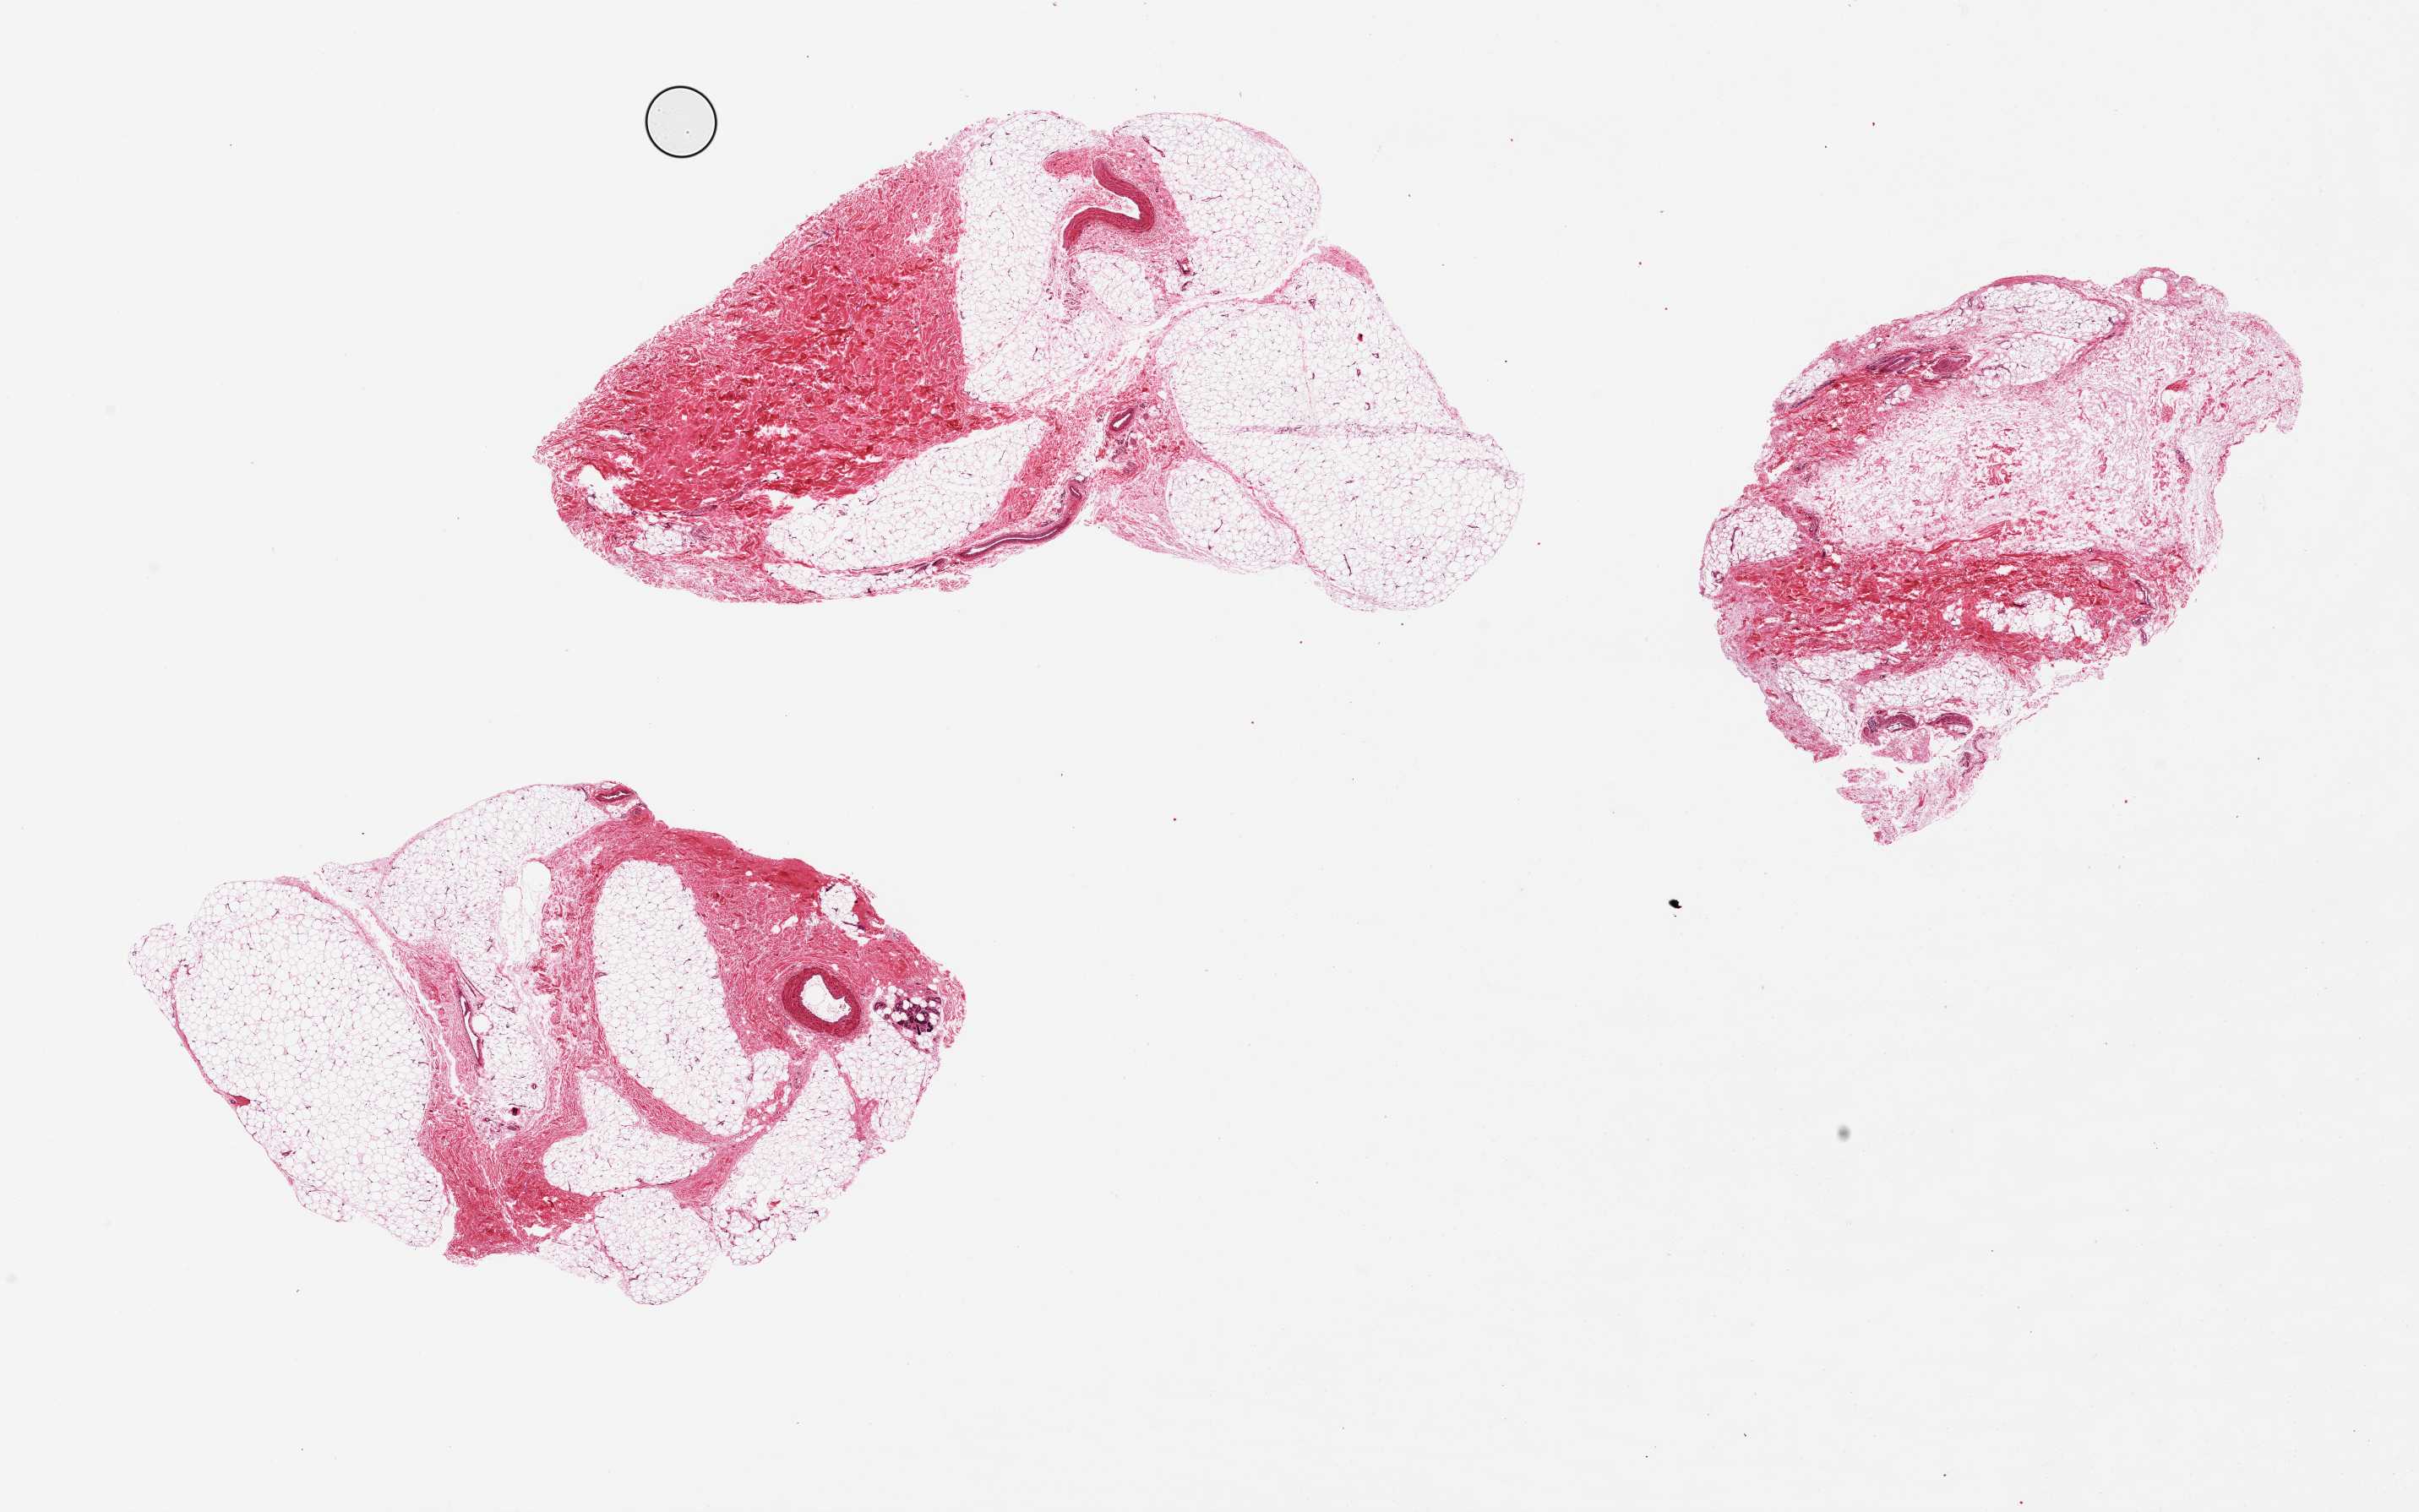
Whole-slide image, H&E stain, brightfield — a low-resolution overview of the entire scanned area, about 22.6 x 14.2 mm (acquisition: 20x scan), PAXgene-fixed paraffin-embedded (PFPE) section, sampled site (target tissue): tibial nerve, tissue donor sample. Donor sex: male.
Review note (as recorded): Pieces of adipose and connective tissue; no nerve present.